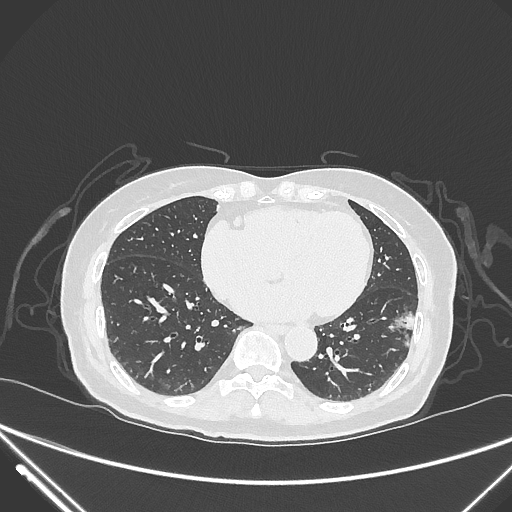
Chest CT, one axial slice. Position 114 of 310 along the scan axis. Reconstruction kernel IMR1,SharpPlus. 120 kVp. Lung window (W 1500 / L -600 HU). 1 mm slice thickness. 512 × 512 image matrix, field of view 377 × 377 mm. Patient: female, 82 years. From the clinical record (not read from this slice): clinical TNM (as recorded): T1c N0 M0.
Annotated regions visible in this slice (bounding box drawn by a radiologist):
- lung tumour (recorded histology: adenocarcinoma): box from (x=386, y=312) to (x=423, y=356) px